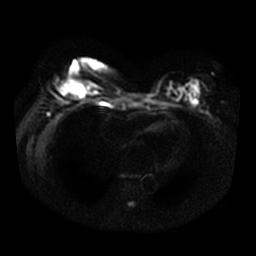
Breast MRI, one axial slice; slice 17 of 34 in the series (ordered by position); diffusion-weighted series; image 2 of 4 stored at this slice position (different b-values; order by instance number); 3 T; 5 mm slice thickness; 256 × 256 image matrix. Female patient.
Structures marked on this image (expert manual segmentation):
- tumour on diffusion-weighted imaging: bounding box [x1, y1, x2, y2] px = [63, 81, 86, 95]